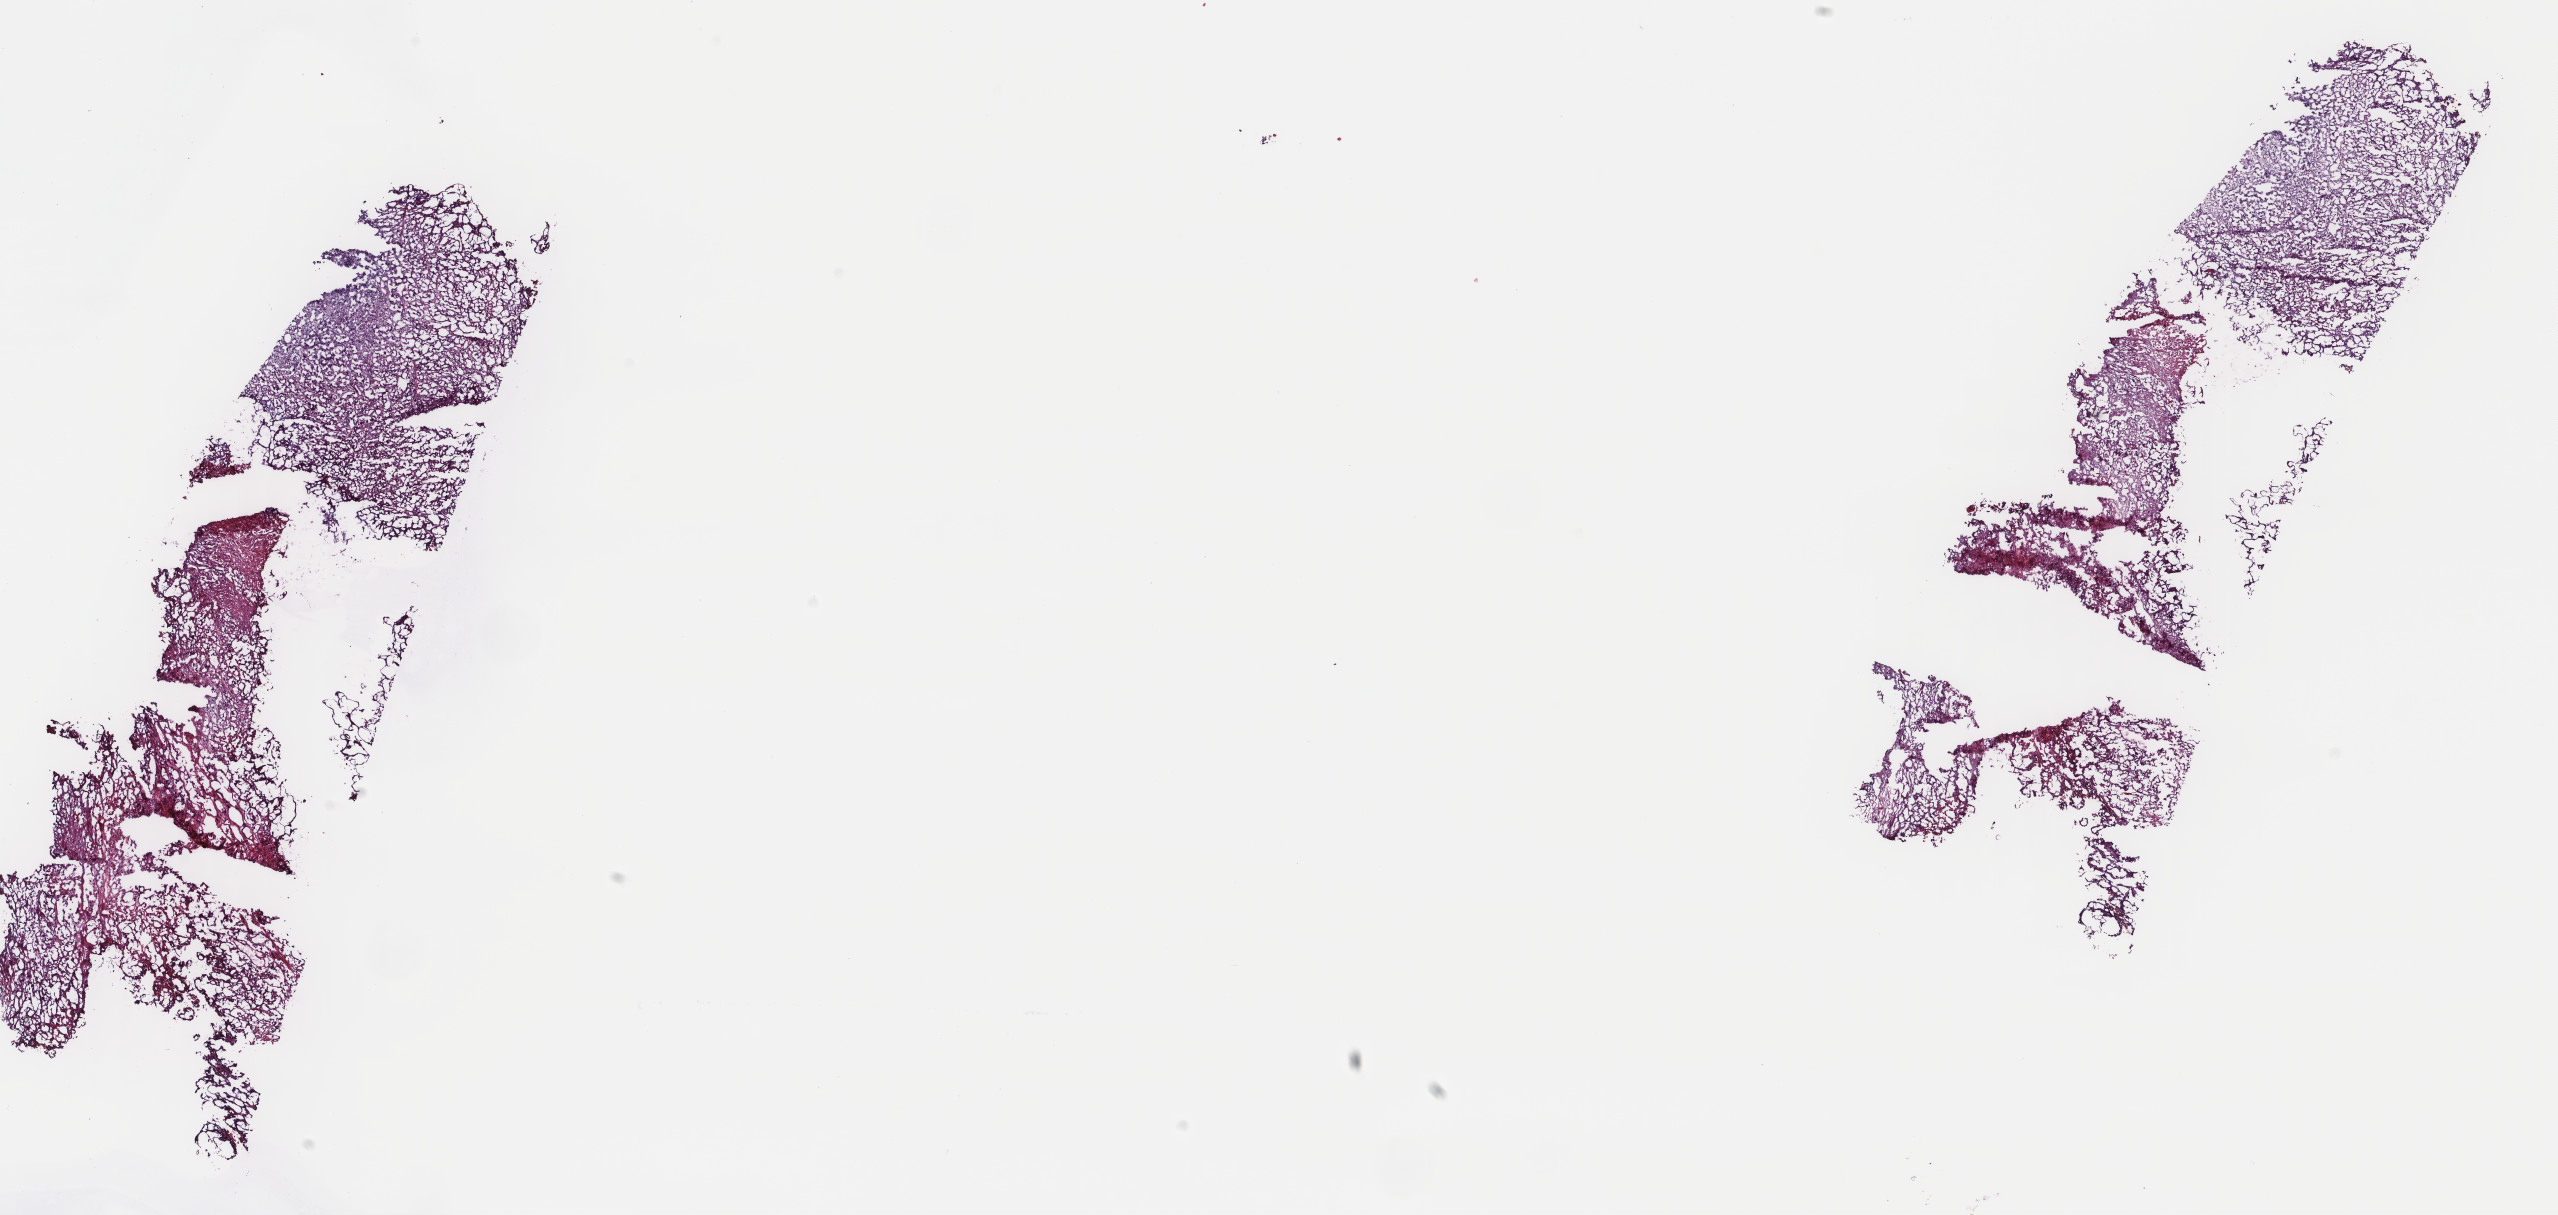
Whole-slide histology image, H&E-stained — shown as a low-resolution overview of the whole scanned area (about 20.3 x 9.6 mm, from a 40x scan); frozen section from the top of the tissue portion; bladder, primary tumour sample. Male, age 50 years at initial diagnosis. Histologic grade: high grade. Pathologist review of this section (percent, as recorded): tumour cells 60%, tumour nuclei 75%, normal cells 0%, stromal cells 25%, necrosis 15%. Infiltration values recorded for this section: lymphocyte infiltration 4%, monocyte infiltration 3%, neutrophil infiltration 0%.
• AJCC pathologic stage: II (6th edition)
• pathologic diagnosis: Transitional cell carcinoma
• TNM: N0 M0